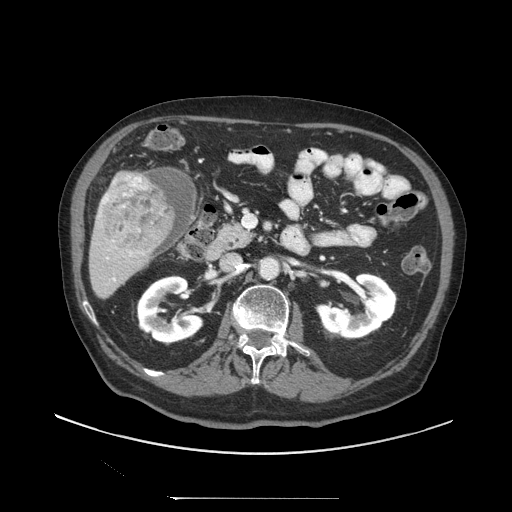
Contrast-enhanced abdominal CT (liver protocol), one axial slice. Slice 38 of 97 in the series (ordered by position). Reconstruction kernel STANDARD. Soft-tissue window (W 400 / L 40 HU). 2.5 mm slice thickness. 512 × 512 image matrix. From the clinical record (not read from this slice): diagnosis: hepatocellular carcinoma (patient treated with transarterial chemoembolisation; whether this scan precedes or follows treatment is not stated here); TNM stage (as recorded): Stage-IIIC; Child-Pugh class: A; tumour differentiation: well differentiated; tumour nodularity: uninodular.
Annotated regions visible in this slice (semi-automatic segmentation, software-assisted and operator-edited):
- liver parenchyma outside the tumour (the mass and vessels are separate outlines, so this box may not span the whole liver): box from (x=88, y=170) to (x=174, y=298) px
- mass: (x=101, y=174)–(x=175, y=252)
- liver vessels: (x=100, y=180)–(x=132, y=281)